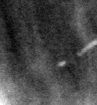
Crop from a digitized film mammogram around one marked abnormality; right breast; MLO view.
- Marked abnormality: calcifications, distribution regional; BI-RADS assessment category 2; benign without callback (not worked up further).